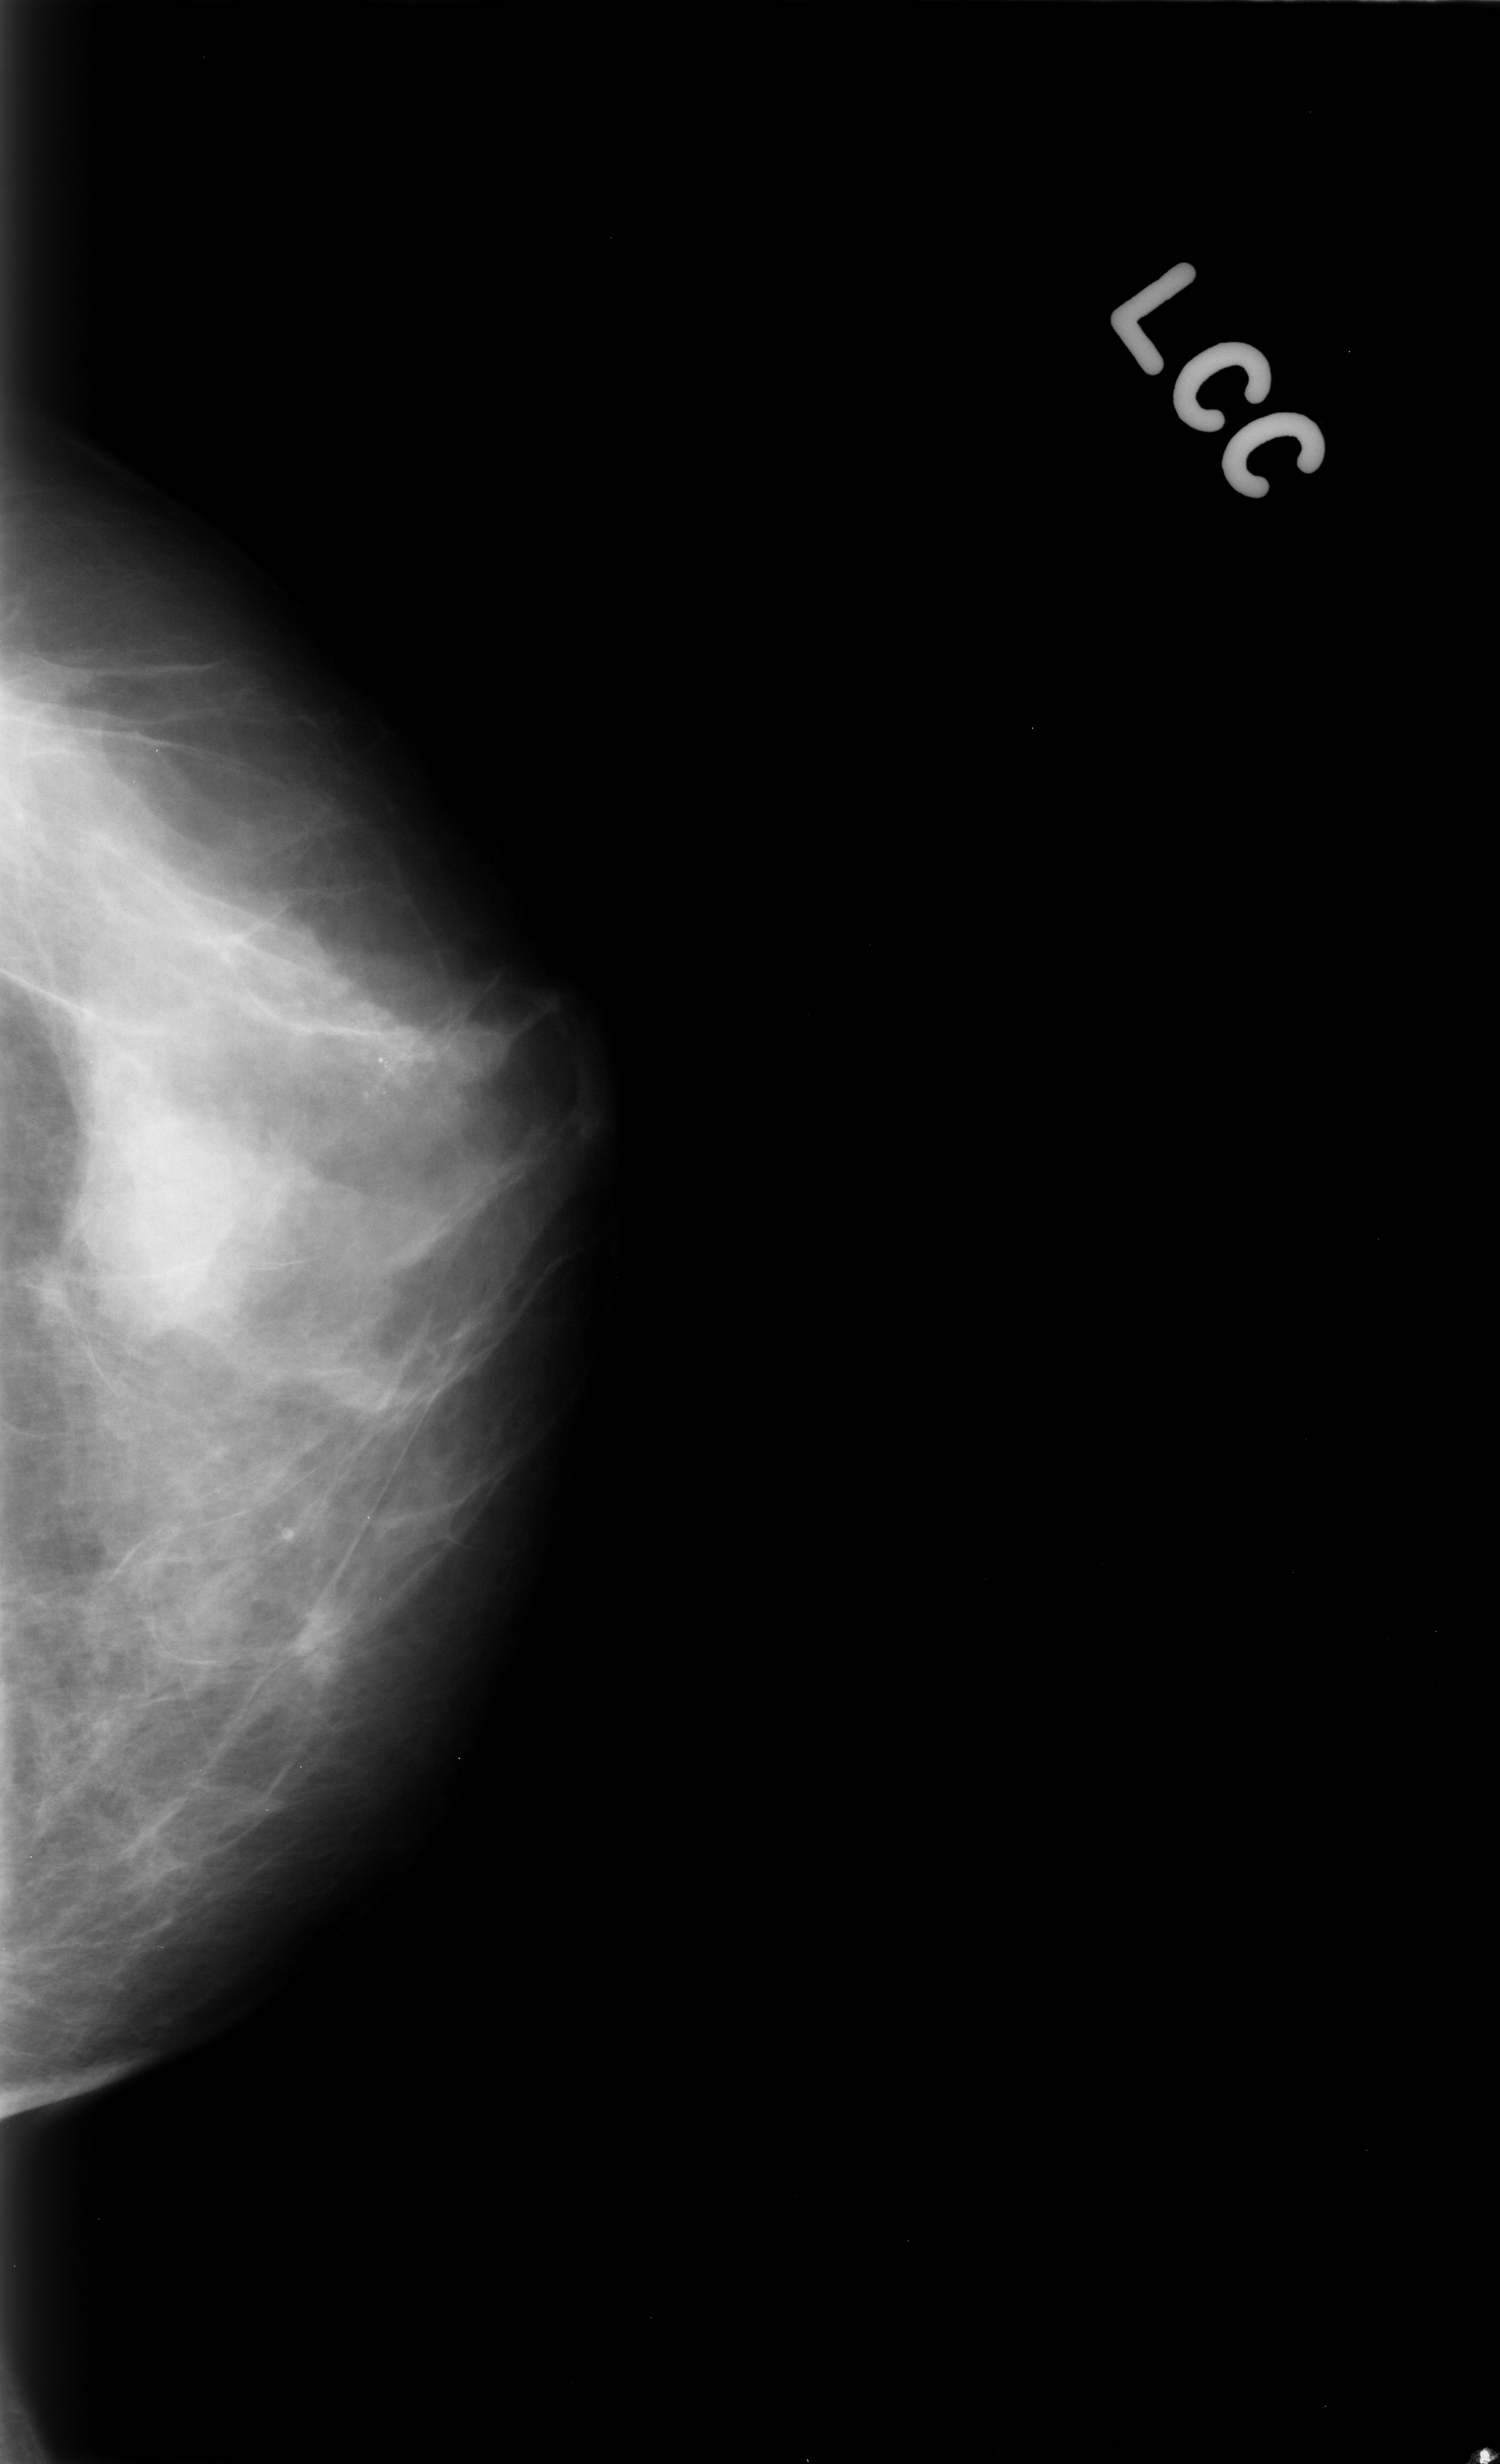
Digitized screen-film mammogram; left breast; craniocaudal (CC) view; BI-RADS breast density category 3 (scale 1–4); 1500 × 2464 image matrix.
Expert-marked regions of interest on this film, with their recorded descriptors:
- calcifications, morphology pleomorphic, distribution clustered; BI-RADS assessment category 4; subtlety rating 3 on a 1 (subtle) to 5 (obvious) scale; pathology (as recorded): benign: bounding box <337,959,464,1116> (left, top, right, bottom; pixels)